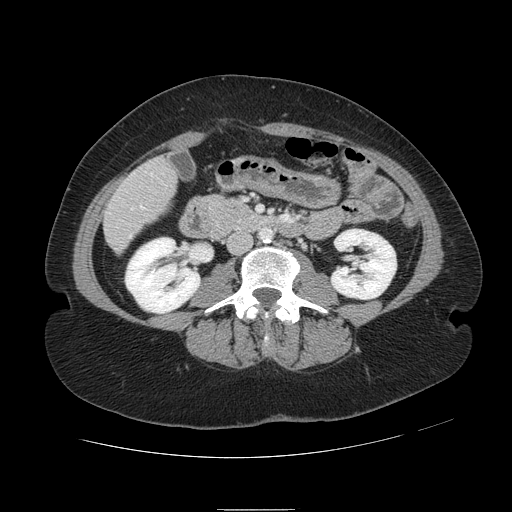
Contrast-enhanced abdominal CT, one axial slice; position 19 of 121 along the scan axis; intravenous contrast given; soft-tissue window (W 400 / L 40 HU); 2.5 mm slice thickness; 512 × 512 image matrix, field of view 400 × 400 mm. Female patient, age 52 years. From the clinical record (not read from this slice): diagnosis: colorectal cancer liver metastases, imaged before liver resection; multiple liver metastases: yes; largest metastasis: 6.3 cm.
Annotated regions visible in this slice (outlined manually by an expert reader):
- hepatic veins: bounding box (x1, y1, x2, y2) in pixels: (141, 173, 153, 209)
- liver: (105, 162, 175, 250)
- portal vein (with intrahepatic branches): (131, 208, 133, 210)